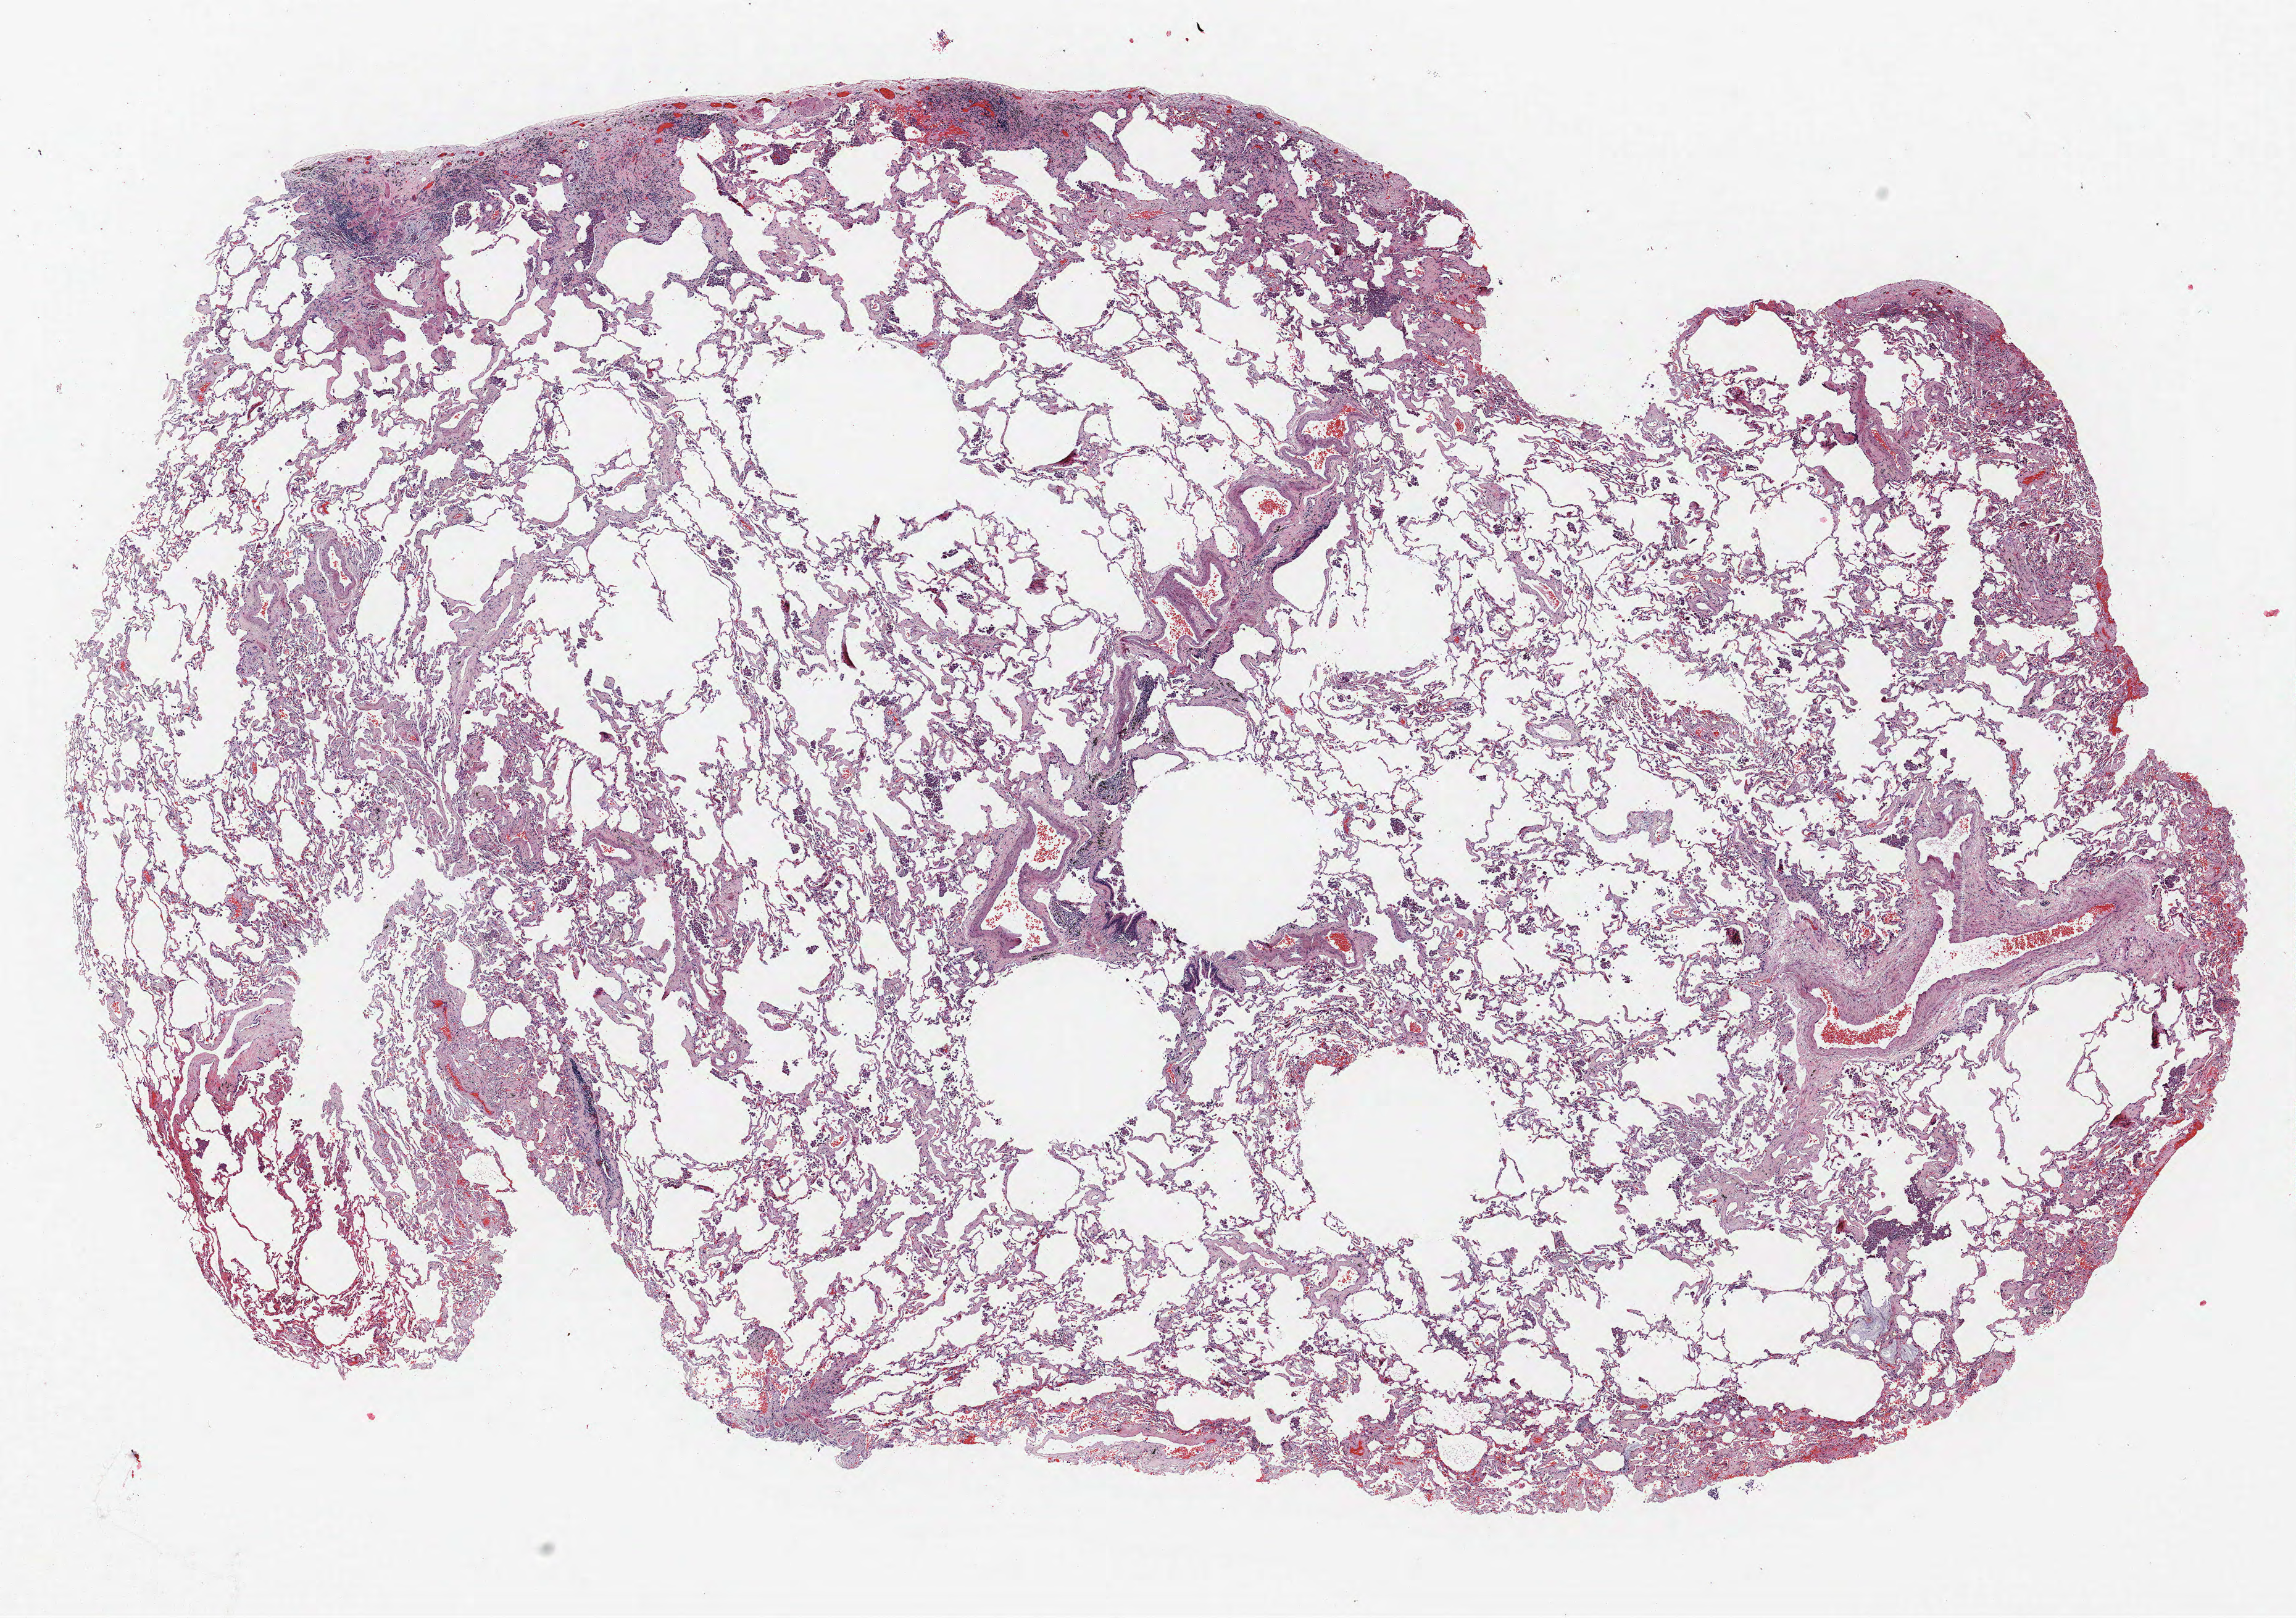
Whole-slide histology image, H&E-stained — whole scanned area (about 14.9 x 10.5 mm, slide scanned at 40x) shown as a low-resolution overview; formalin-fixed paraffin-embedded (FFPE) section; lung. Male patient, aged 61 at enrolment. Current smoker at enrolment. Grade: poorly differentiated (G3).
Tumour size (pathology): 12 mm. ICD-O-3 topography: upper lobe of lung (C34.1). Participant's lung-cancer diagnosis: Squamous cell carcinoma, NOS. Stage (AJCC 6th edition): IIIB. Primary tumour location (clinical record): right upper lobe.